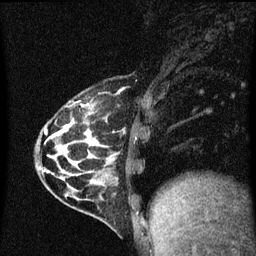
Breast MRI (dynamic contrast-enhanced), one sagittal slice. Position 19 of 60 along the scan axis. Dynamic contrast-enhanced series, image 2 of 3 at this slice position (ordered by acquisition). 1.5 T. TE 4.2 ms, TR 8.4 ms. 256 × 256 image matrix. Female patient, age 32 years.
Outlined on this slice (semi-automatically segmented with operator editing):
- analysis volume of interest (the breast-tissue region the enhancement analysis was run in; not a lesion): bounding box <37,90,151,169> (left, top, right, bottom; pixels)
- tumour enhancement mask (voxels above the 70 % enhancement threshold inside the analysis volume of interest): <46,130,48,133>